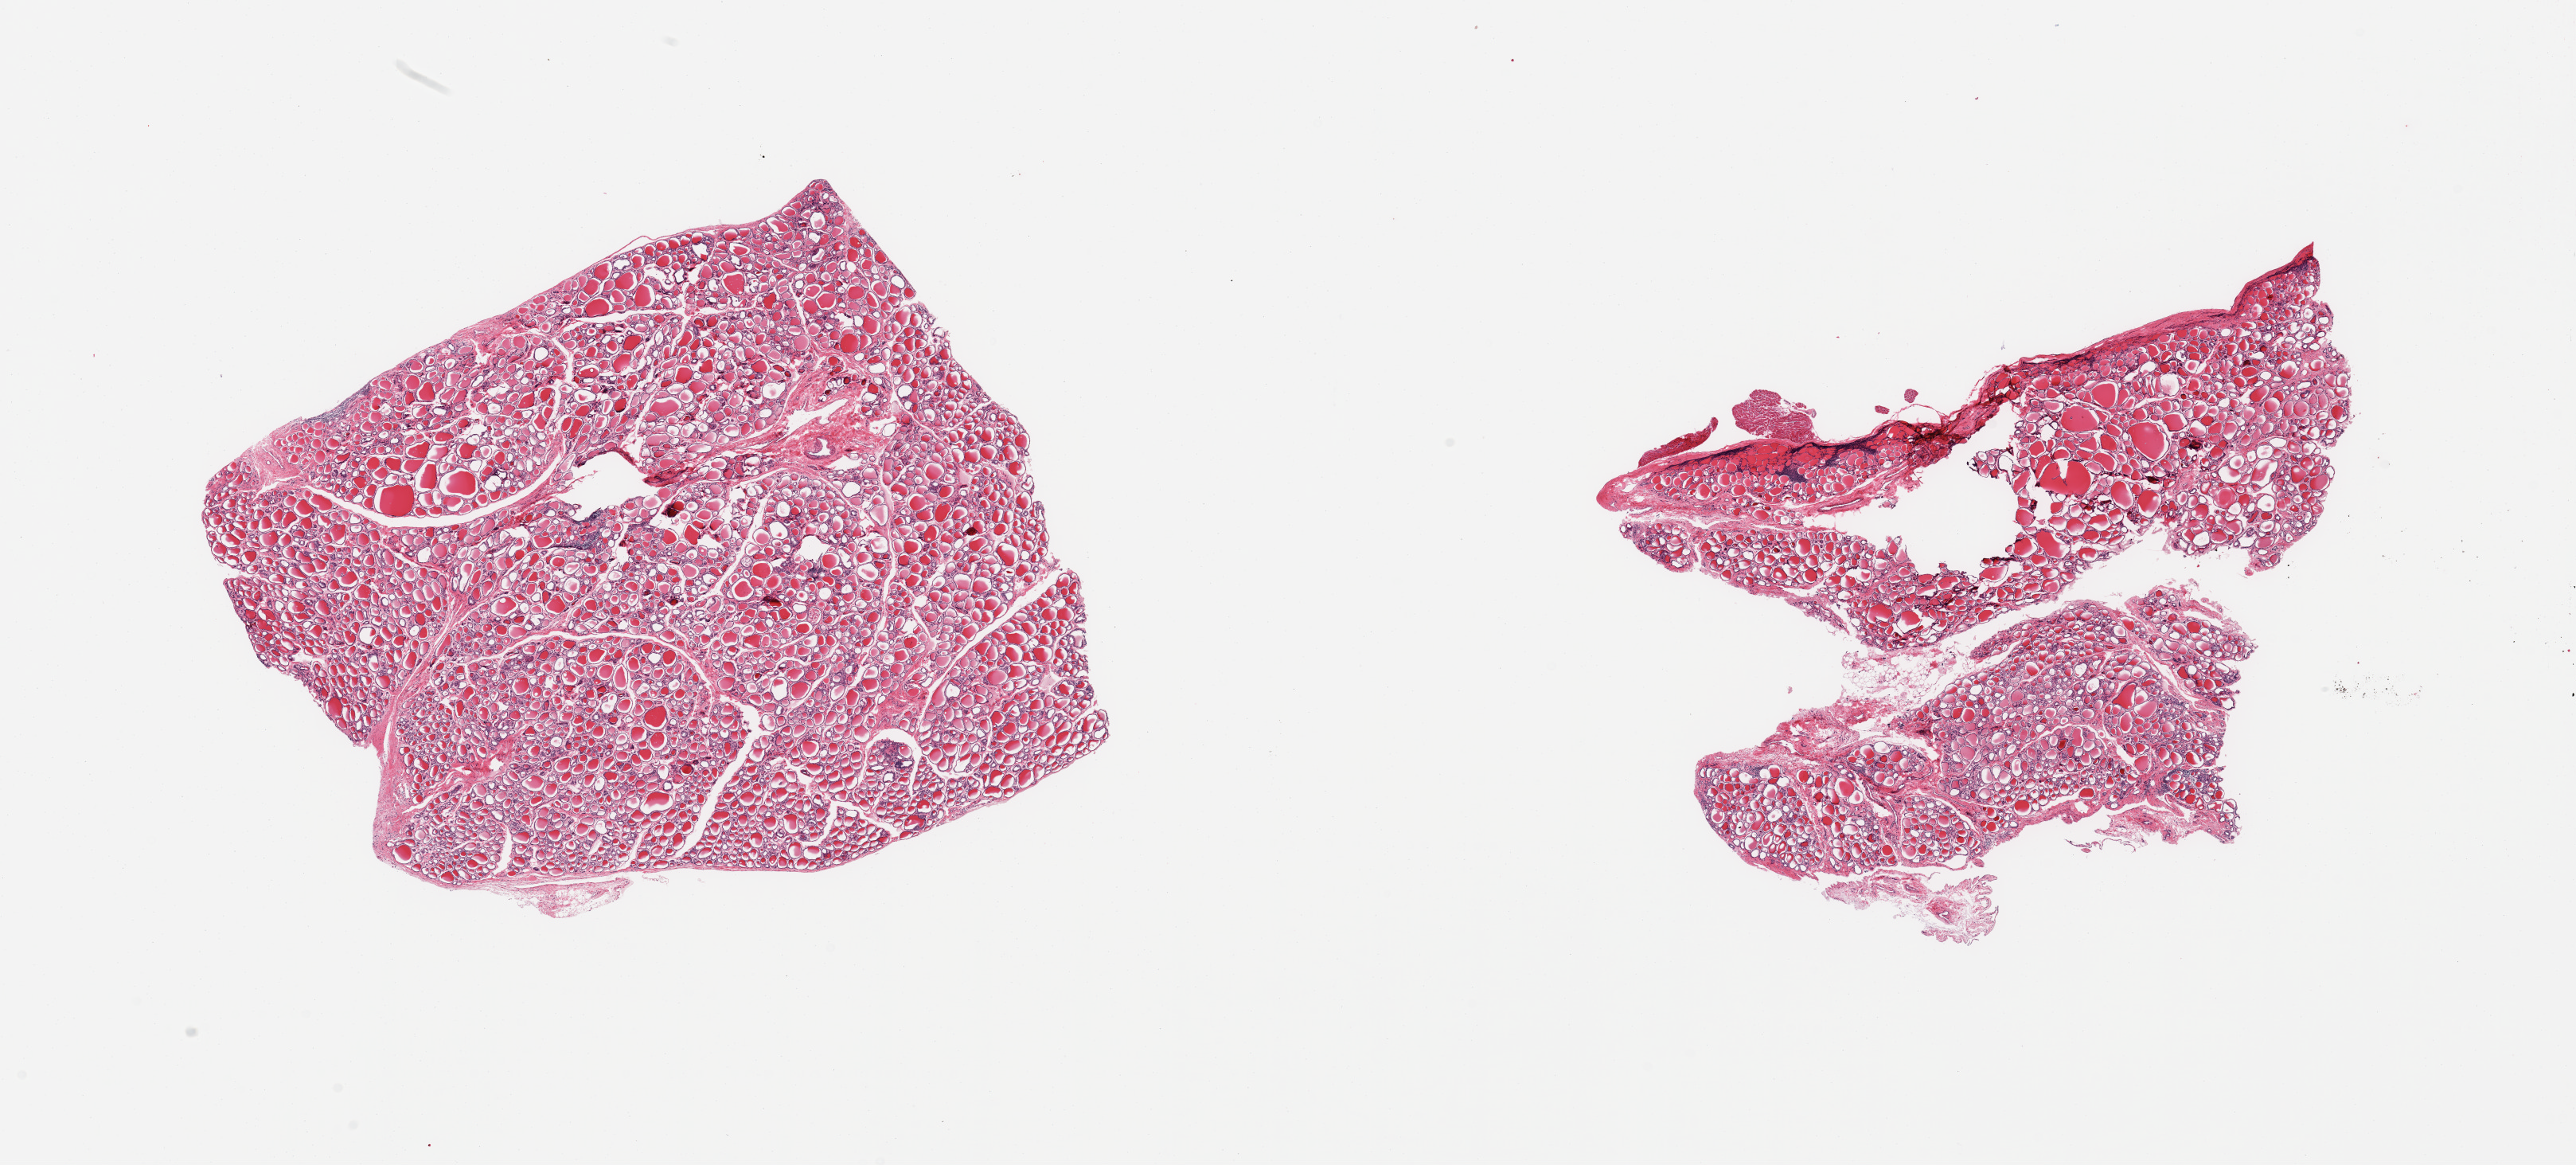
Digitized hematoxylin and eosin (H&E)-stained section, brightfield, a low-resolution overview of the entire scanned area, about 25.6 x 11.6 mm (from a 20x scan); PAXgene-fixed, paraffin-embedded tissue; section of thyroid (target tissue); tissue donor sample. Female donor.
Review note (as recorded): 2 pieces: focus of lymphocytes, detached fragments of myocardium.